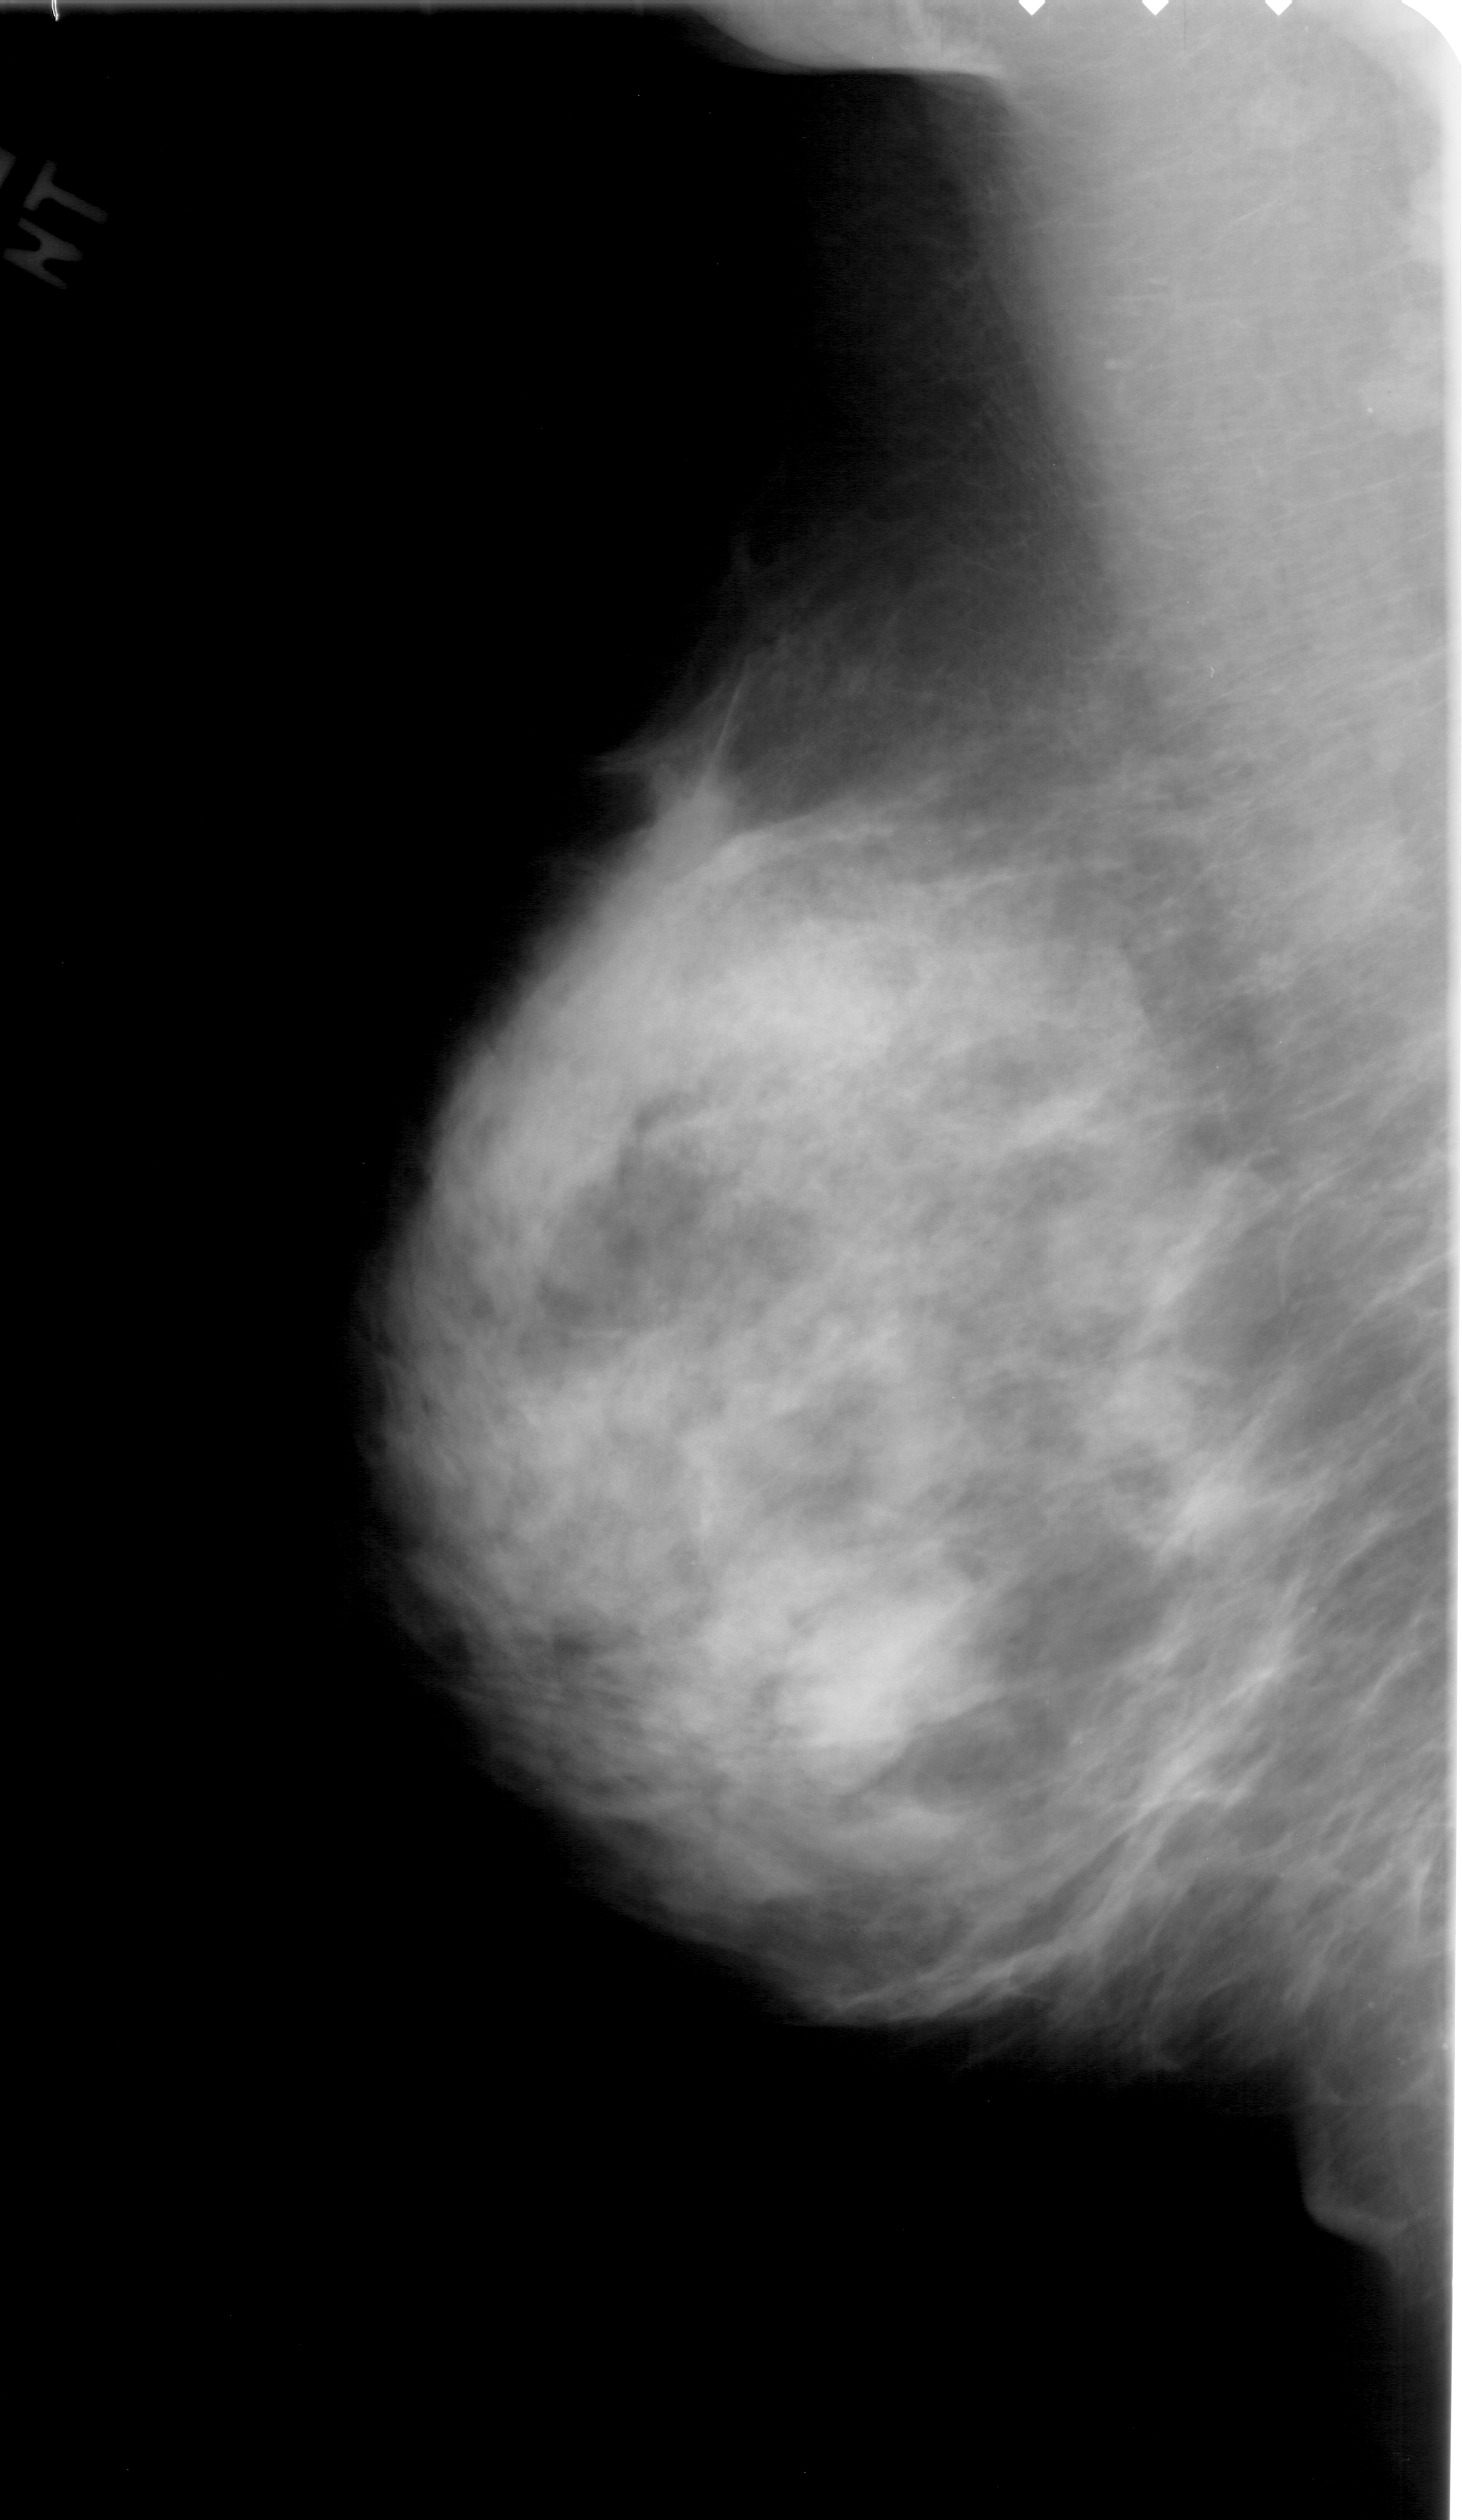
Scanned film-screen mammogram. Left breast. Mediolateral oblique (MLO) view. BI-RADS breast density category 3 (scale 1–4). 1462 × 2520 image matrix.
Expert-marked regions of interest on this image (one box per marked abnormality):
- mass, shape lobulated, margins obscured; BI-RADS assessment category 4; subtlety rating 2 on a 1 (subtle) to 5 (obvious) scale; pathology result (as recorded, not read from the image): benign: bounding box (x1, y1, x2, y2) in pixels: (771, 1595, 963, 1784)